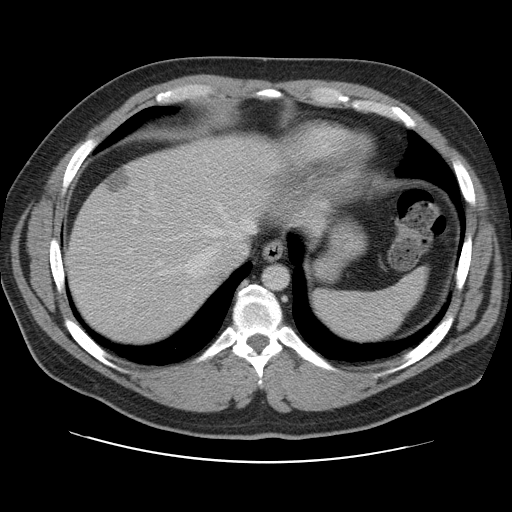
Contrast-enhanced abdominal CT, one axial slice. Slice 92 of 109 in the series (ordered by position). Intravenous contrast given. Soft-tissue window (W 400 / L 40 HU). 512 × 512 image matrix, field of view 402 × 402 mm. Male patient, age 35 years. From the clinical record (not read from this slice): diagnosis: colorectal cancer liver metastases, imaged before liver resection; multiple liver metastases: yes; largest metastasis: 2.8 cm.
Annotated regions visible in this slice (manually delineated by an expert):
- hepatic veins: bounding box (x1, y1, x2, y2) in pixels: (158, 188, 254, 294)
- liver: (68, 136, 305, 344)
- planned liver remnant (the part of the liver to remain after resection): (68, 136, 296, 343)
- liver metastasis: (105, 170, 131, 193)